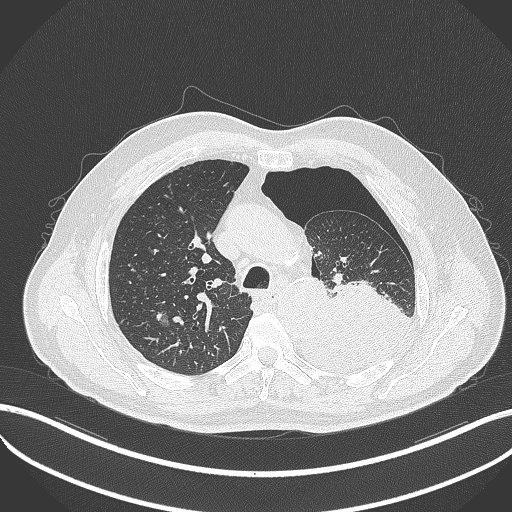
Chest CT, one axial slice. Position 363 of 464 along the scan axis. Reconstruction kernel B70f. Lung window (W 1500 / L -600 HU). 1 mm slice thickness. 512 × 512 image matrix, field of view 400 × 400 mm. Patient: male, 76 years. Case-level facts recorded for this patient, not image findings: clinical TNM (as recorded): T3 N0 M1b.
Annotated regions visible in this slice (bounding box drawn by a radiologist):
- lung tumour (recorded histology: adenocarcinoma): bounding box <296,276,416,374> (left, top, right, bottom; pixels)